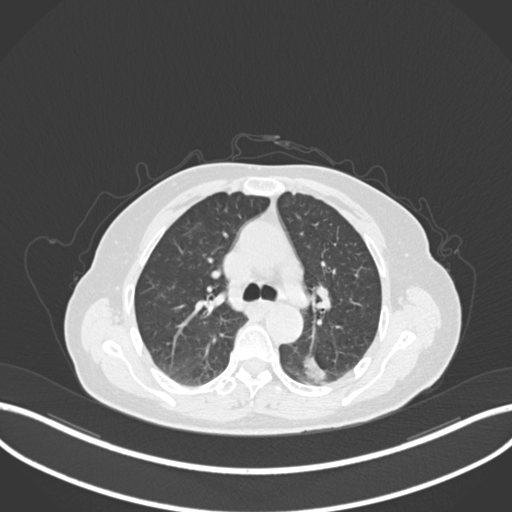
Chest CT, one axial slice; position 543 of 727 along the scan axis; reconstruction kernel B30f; lung window (W 1500 / L -600 HU); 1 mm slice thickness; 512 × 512 image matrix, field of view 400 × 400 mm. Patient: female, 70 years. From the clinical record (not read from this slice): clinical TNM (as recorded): T1c N0 M0.
Annotated regions visible in this slice (bounding box drawn by a radiologist):
- lung tumour (recorded histology: adenocarcinoma): bounding box <303,354,333,385> (left, top, right, bottom; pixels)